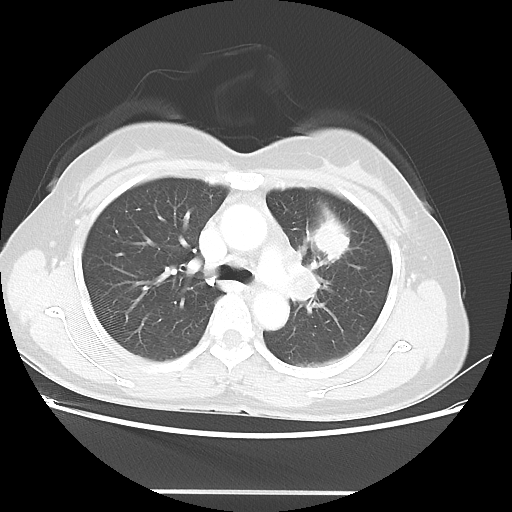
Chest CT, one axial slice. Position 30 of 46 along the scan axis. Reconstruction kernel LUNG. 100 kVp. Lung window (W 1500 / L -600 HU). 5 mm slice thickness. 512 × 512 image matrix, field of view 360 × 360 mm. Patient: female, 50 years. From the clinical record (not read from this slice): clinical TNM (as recorded): T1c N1 M0; histopathological grade: G3.
Structures marked on this image (bounding box drawn by a radiologist):
- lung tumour (recorded histology: adenocarcinoma): bounding box (x1, y1, x2, y2) in pixels: (309, 214, 351, 262)